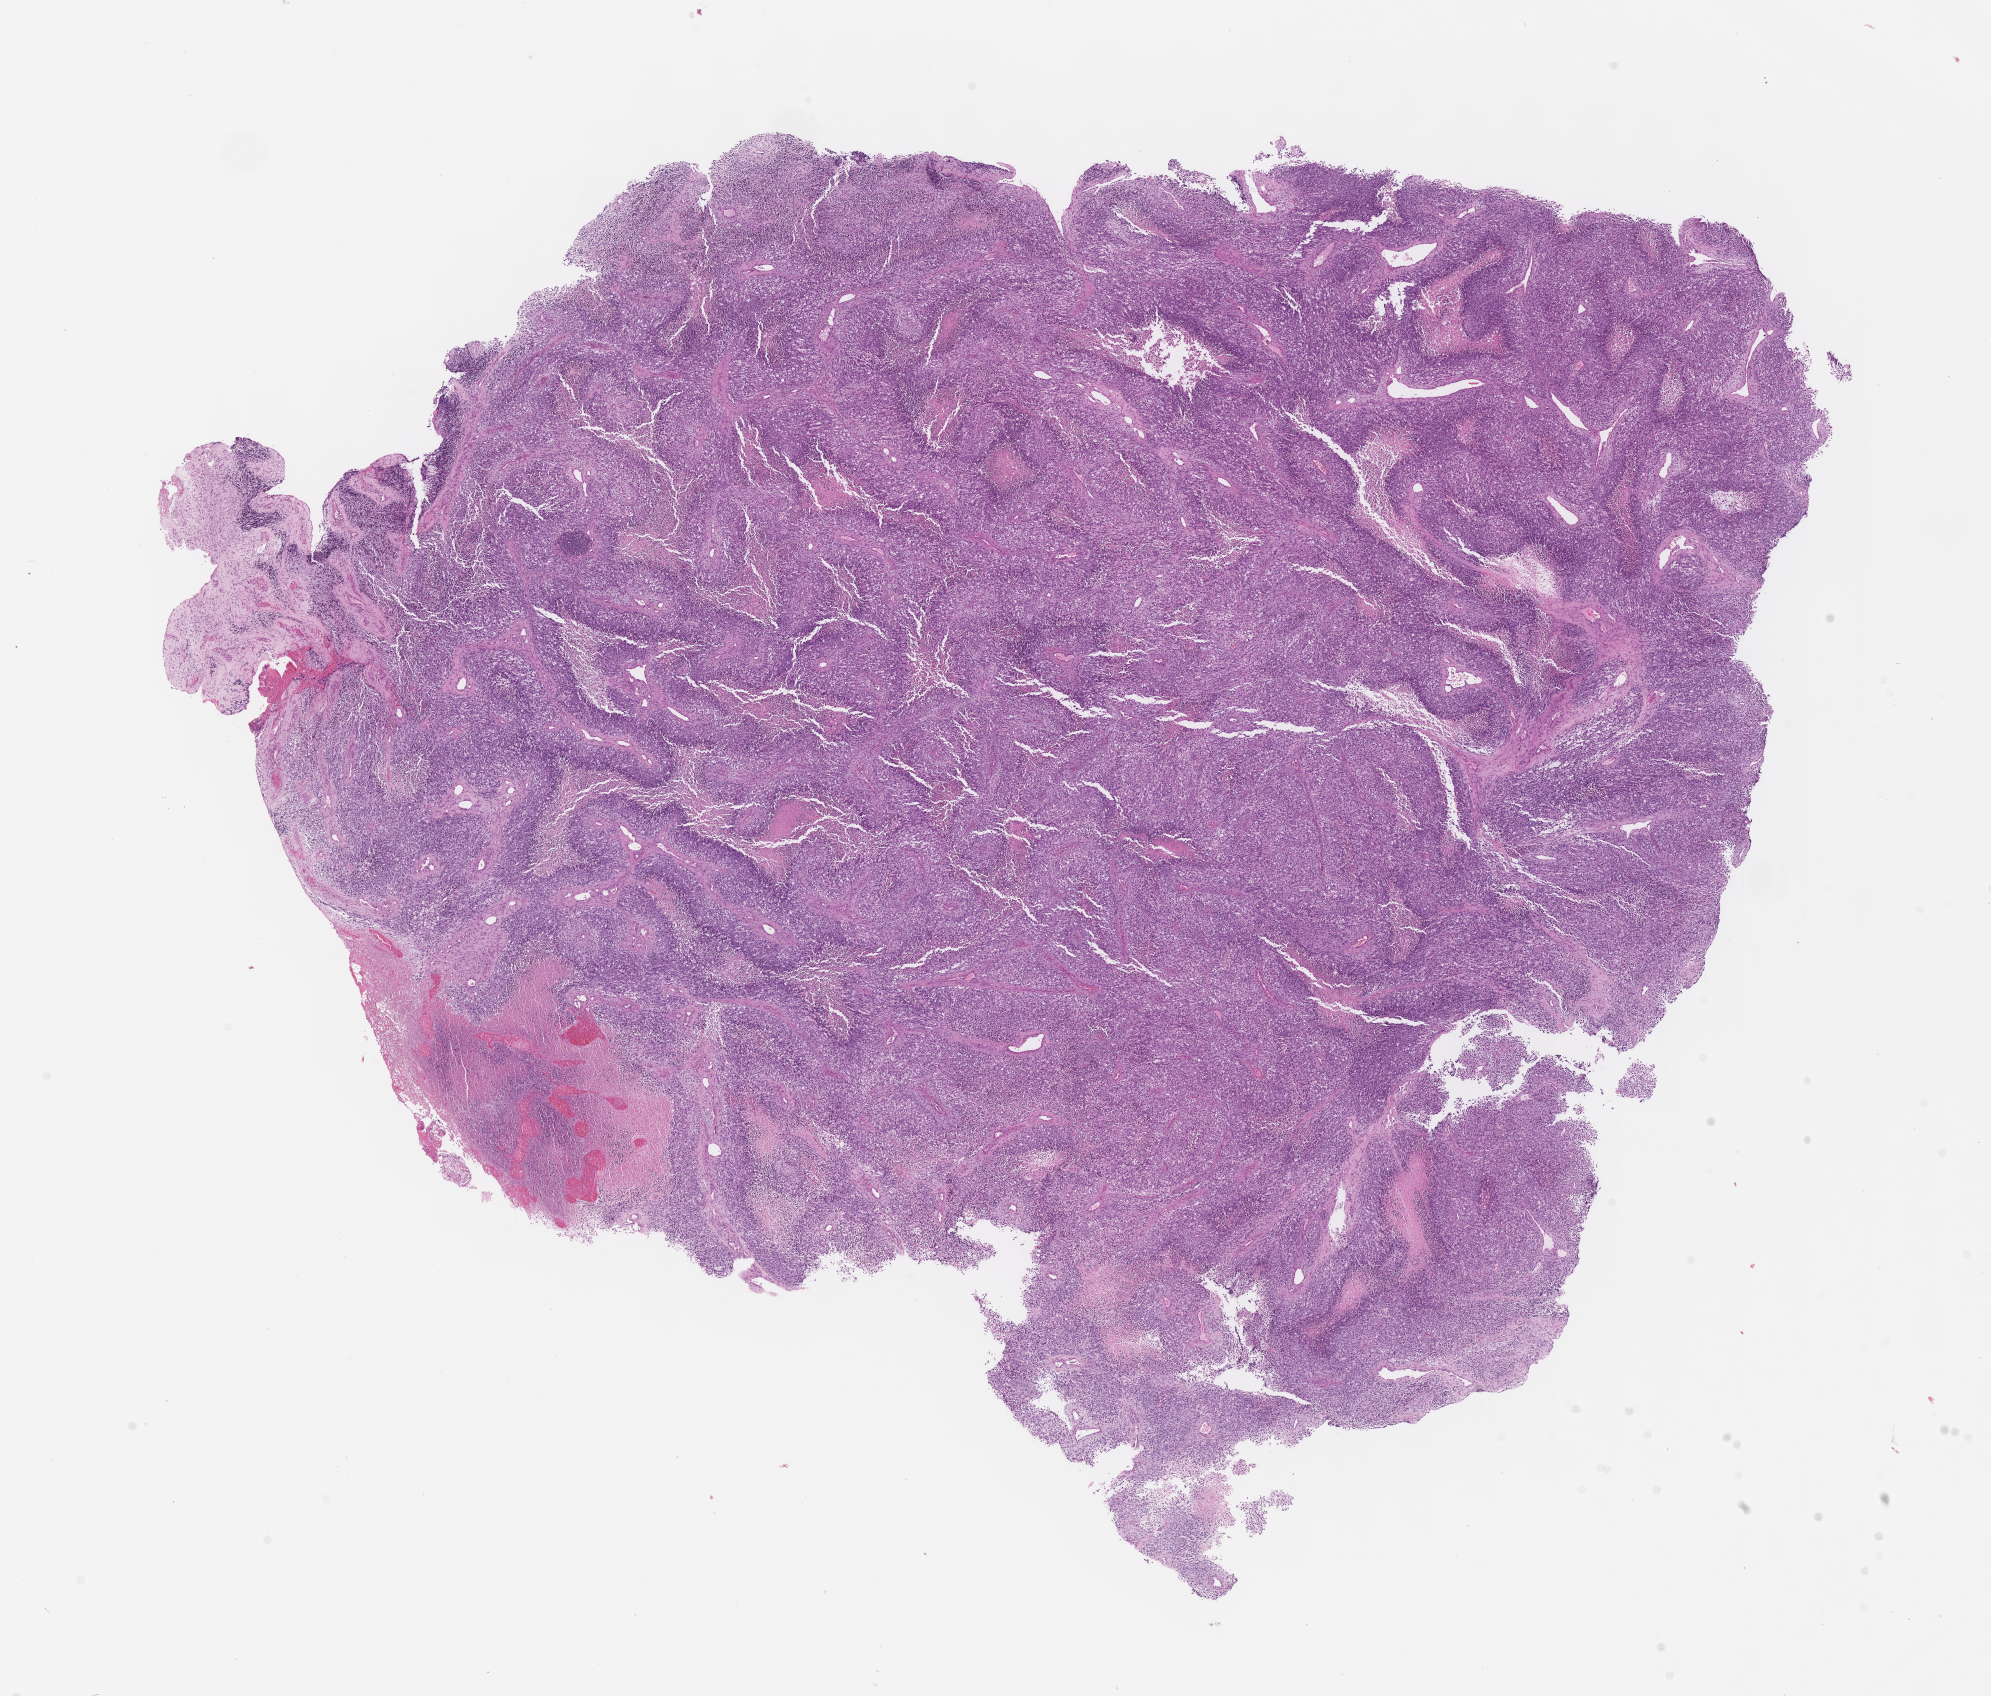
Hematoxylin and eosin (H&E) whole-slide image of tumor tissue, a low-resolution overview of the entire scanned area, about 16.1 x 13.7 mm. FFPE section. Site: paratesticular. Patient: male, age 26.3 years at diagnosis.
* primary site (case record): testis-Paratestis
* diagnosis: rhabdomyosarcoma; histological classification: embryonal rhabdomyosarcoma
* metastatic status at presentation (as recorded): metastatic
* stage (as recorded): 4